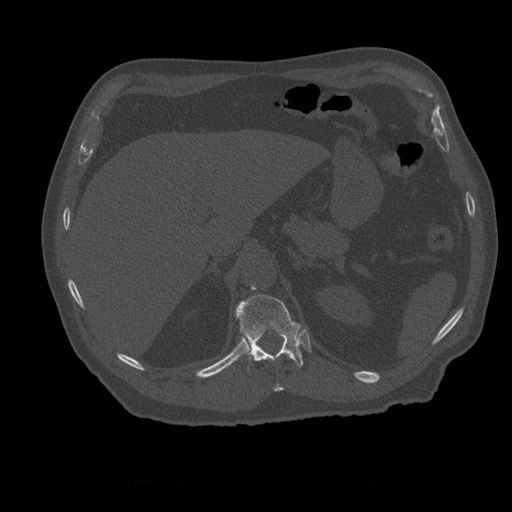
CT including the spine, one axial slice. Slice 263 of 399 in the series (ordered by position). Bone window (W 1800 / L 400 HU). 1.25 mm slice thickness. 512 × 512 image matrix. Patient age 73 years. Case-level facts recorded for this patient, not image findings: primary cancer: prostate; vertebrae with lytic lesions (as recorded): L2.
Outlined on this slice (semi-automatic segmentation, software-assisted and operator-edited):
- T11 vertebra: bounding box [x1, y1, x2, y2] px = [263, 359, 284, 392]
- T12 vertebra: [235, 295, 304, 368]